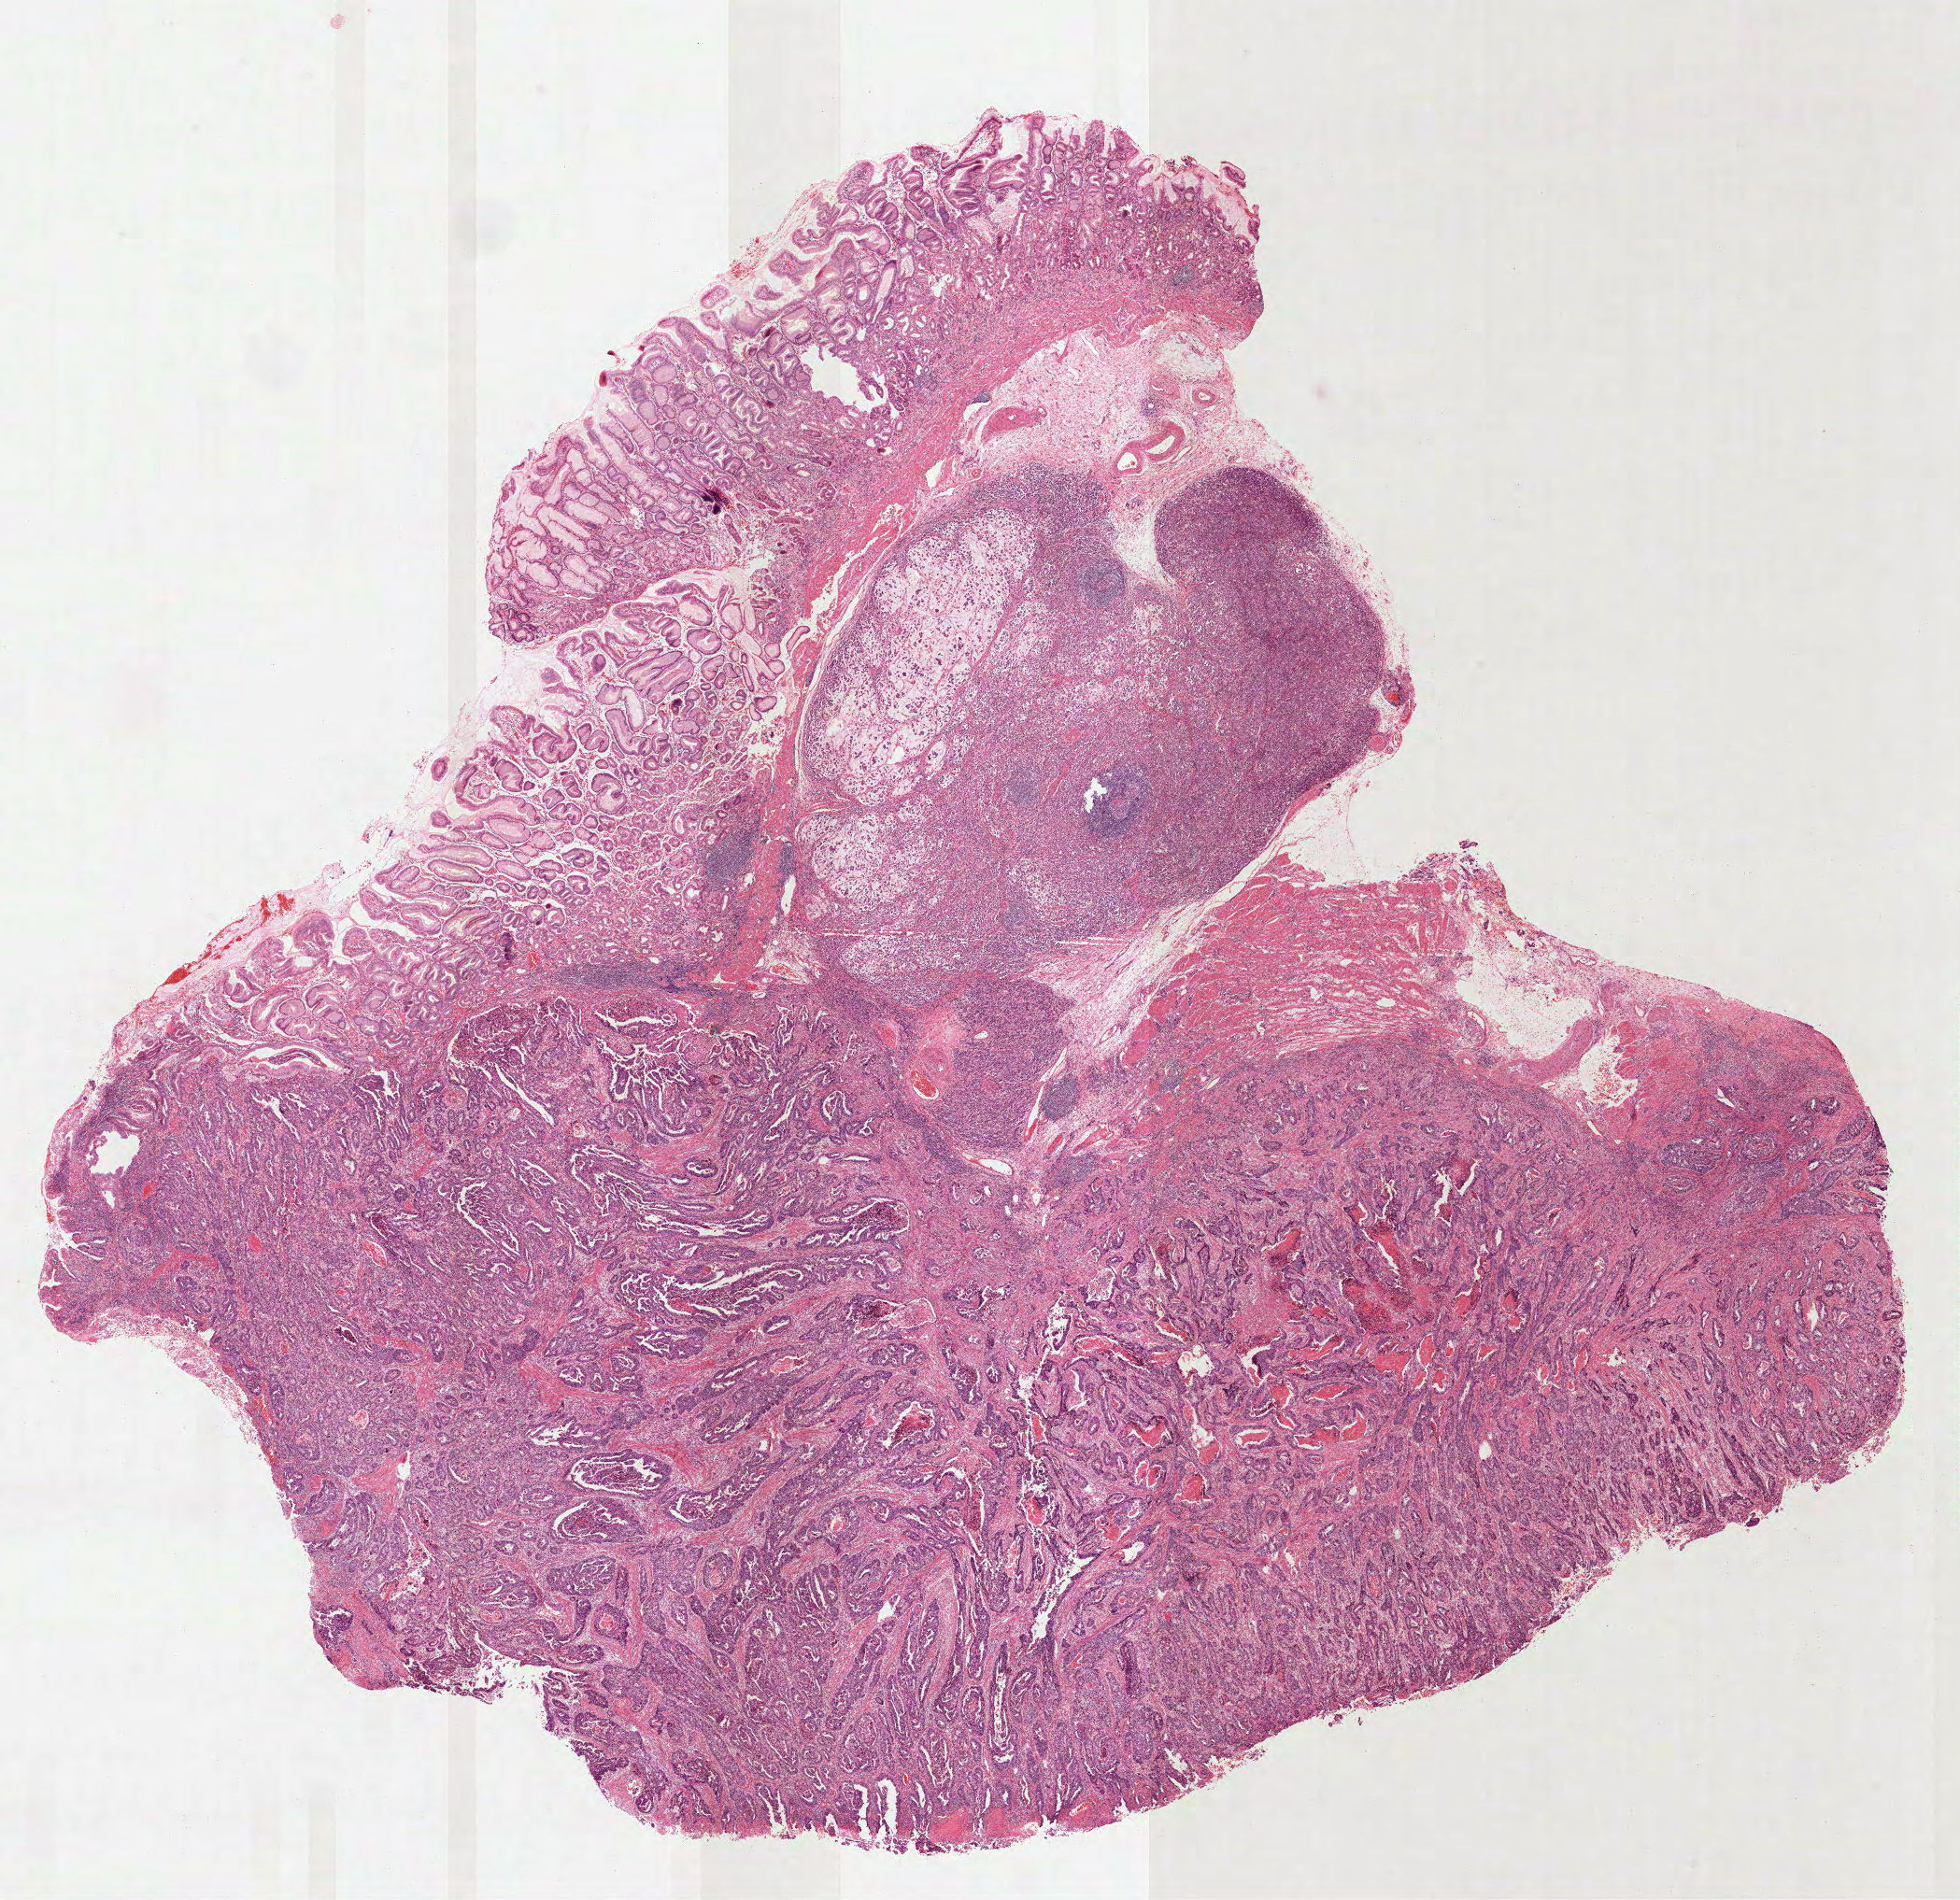
Whole-slide histology image, H&E-stained — shown as a low-resolution overview of the whole scanned area (about 16.9 x 16.4 mm); formalin-fixed paraffin-embedded (FFPE) diagnostic section; sample: primary tumour, stomach. Patient: female, age at initial diagnosis 68 years. Histologic grade: G3 (poorly differentiated).
Diagnosis: Adenocarcinoma, NOS. Lymph nodes positive (case pathology): 7 of 13 examined. AJCC pathologic stage: IIIC (7th edition).